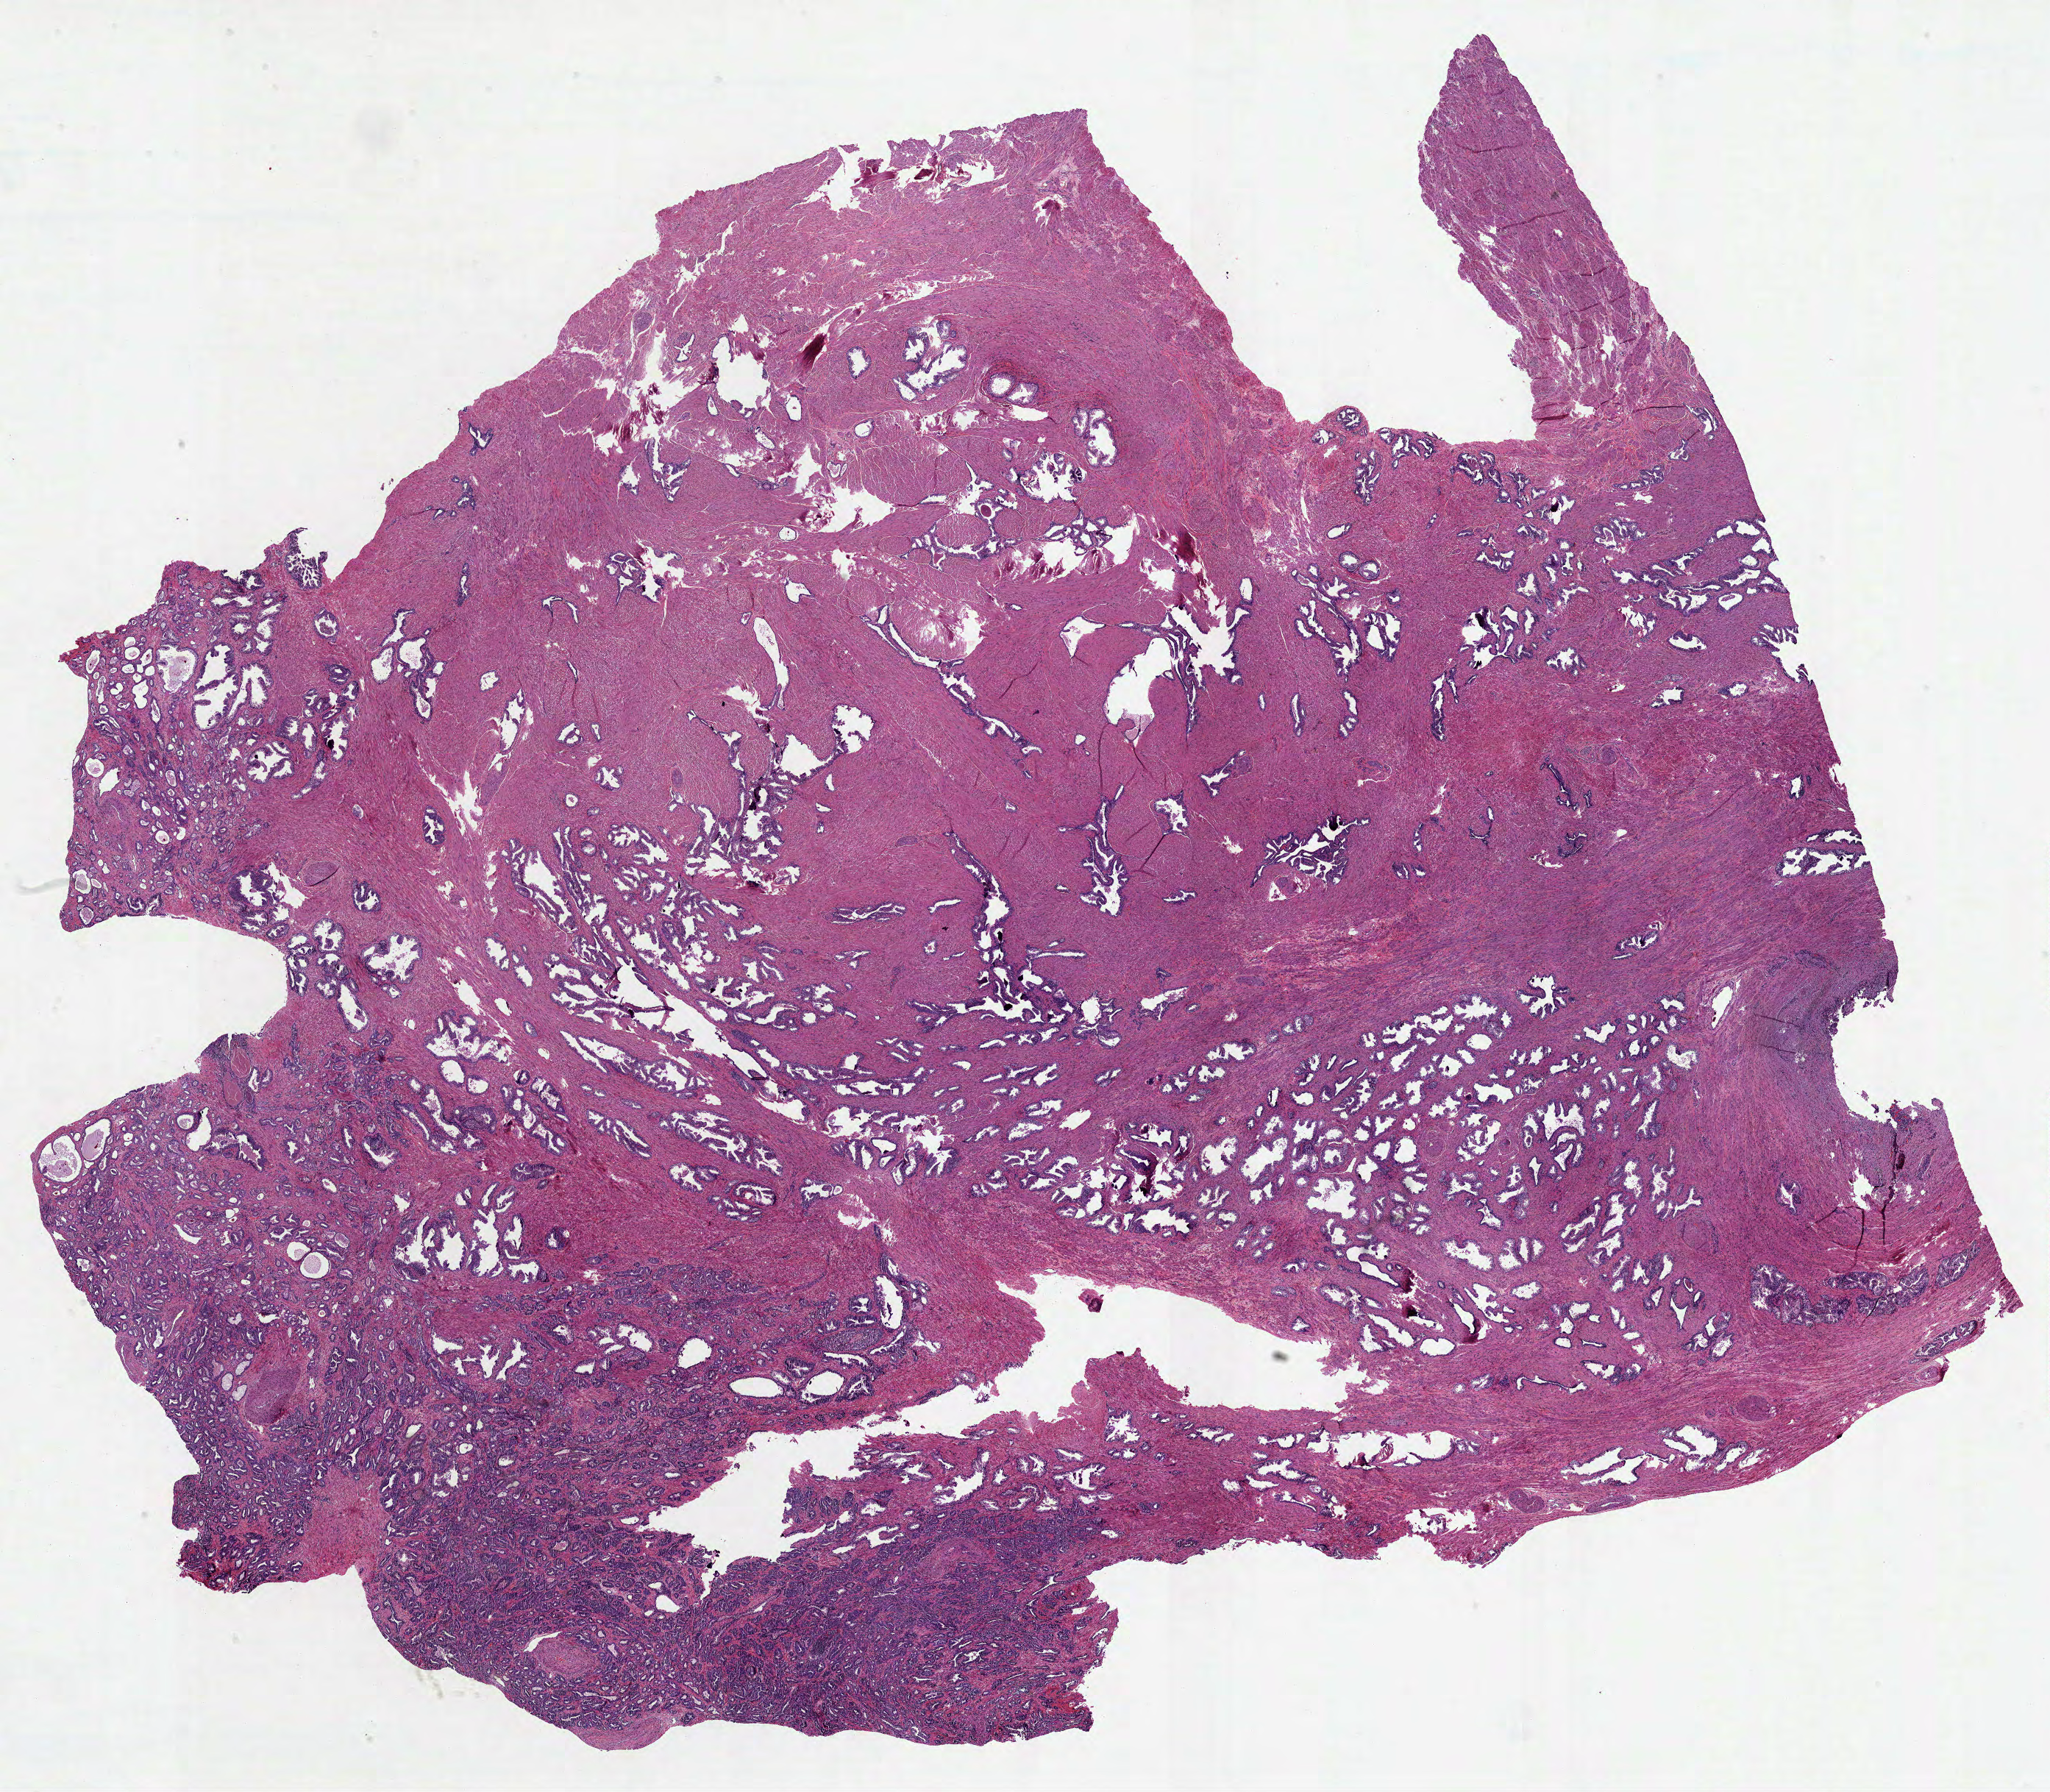
H&E-stained whole-slide image — shown as a low-resolution overview of the whole scanned area (about 22.5 x 19.6 mm); formalin-fixed paraffin-embedded (FFPE) diagnostic section; primary tumour sample from the prostate. Male, age 54 years at initial diagnosis. Gleason score: 7 (3+4).
Lymph nodes positive (case pathology): 0 of 7 examined. Histologic diagnosis: Acinar cell carcinoma (prostate gland).